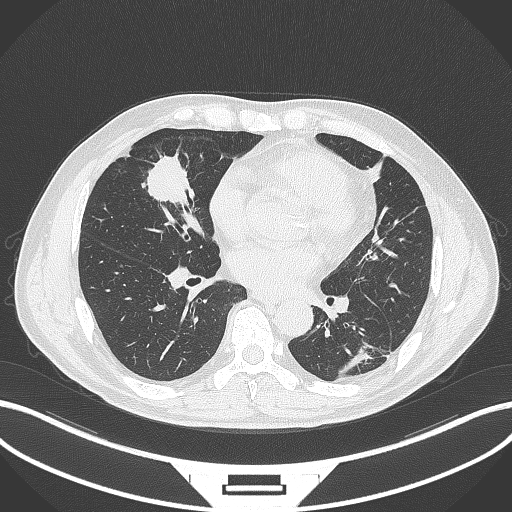
Chest CT, one axial slice. Position 130 of 399 along the scan axis. Reconstruction kernel B70f. 120 kVp. Lung window (W 1500 / L -600 HU). 1 mm slice thickness. 512 × 512 image matrix, field of view 400 × 400 mm. Patient: male, 59 years. Case-level facts recorded for this patient, not image findings: clinical TNM (as recorded): T2a N1 M0.
Annotated regions visible in this slice (rectangle marked by the reading radiologist):
- lung tumour (recorded histology: adenocarcinoma): bounding box <144,151,197,211> (left, top, right, bottom; pixels)